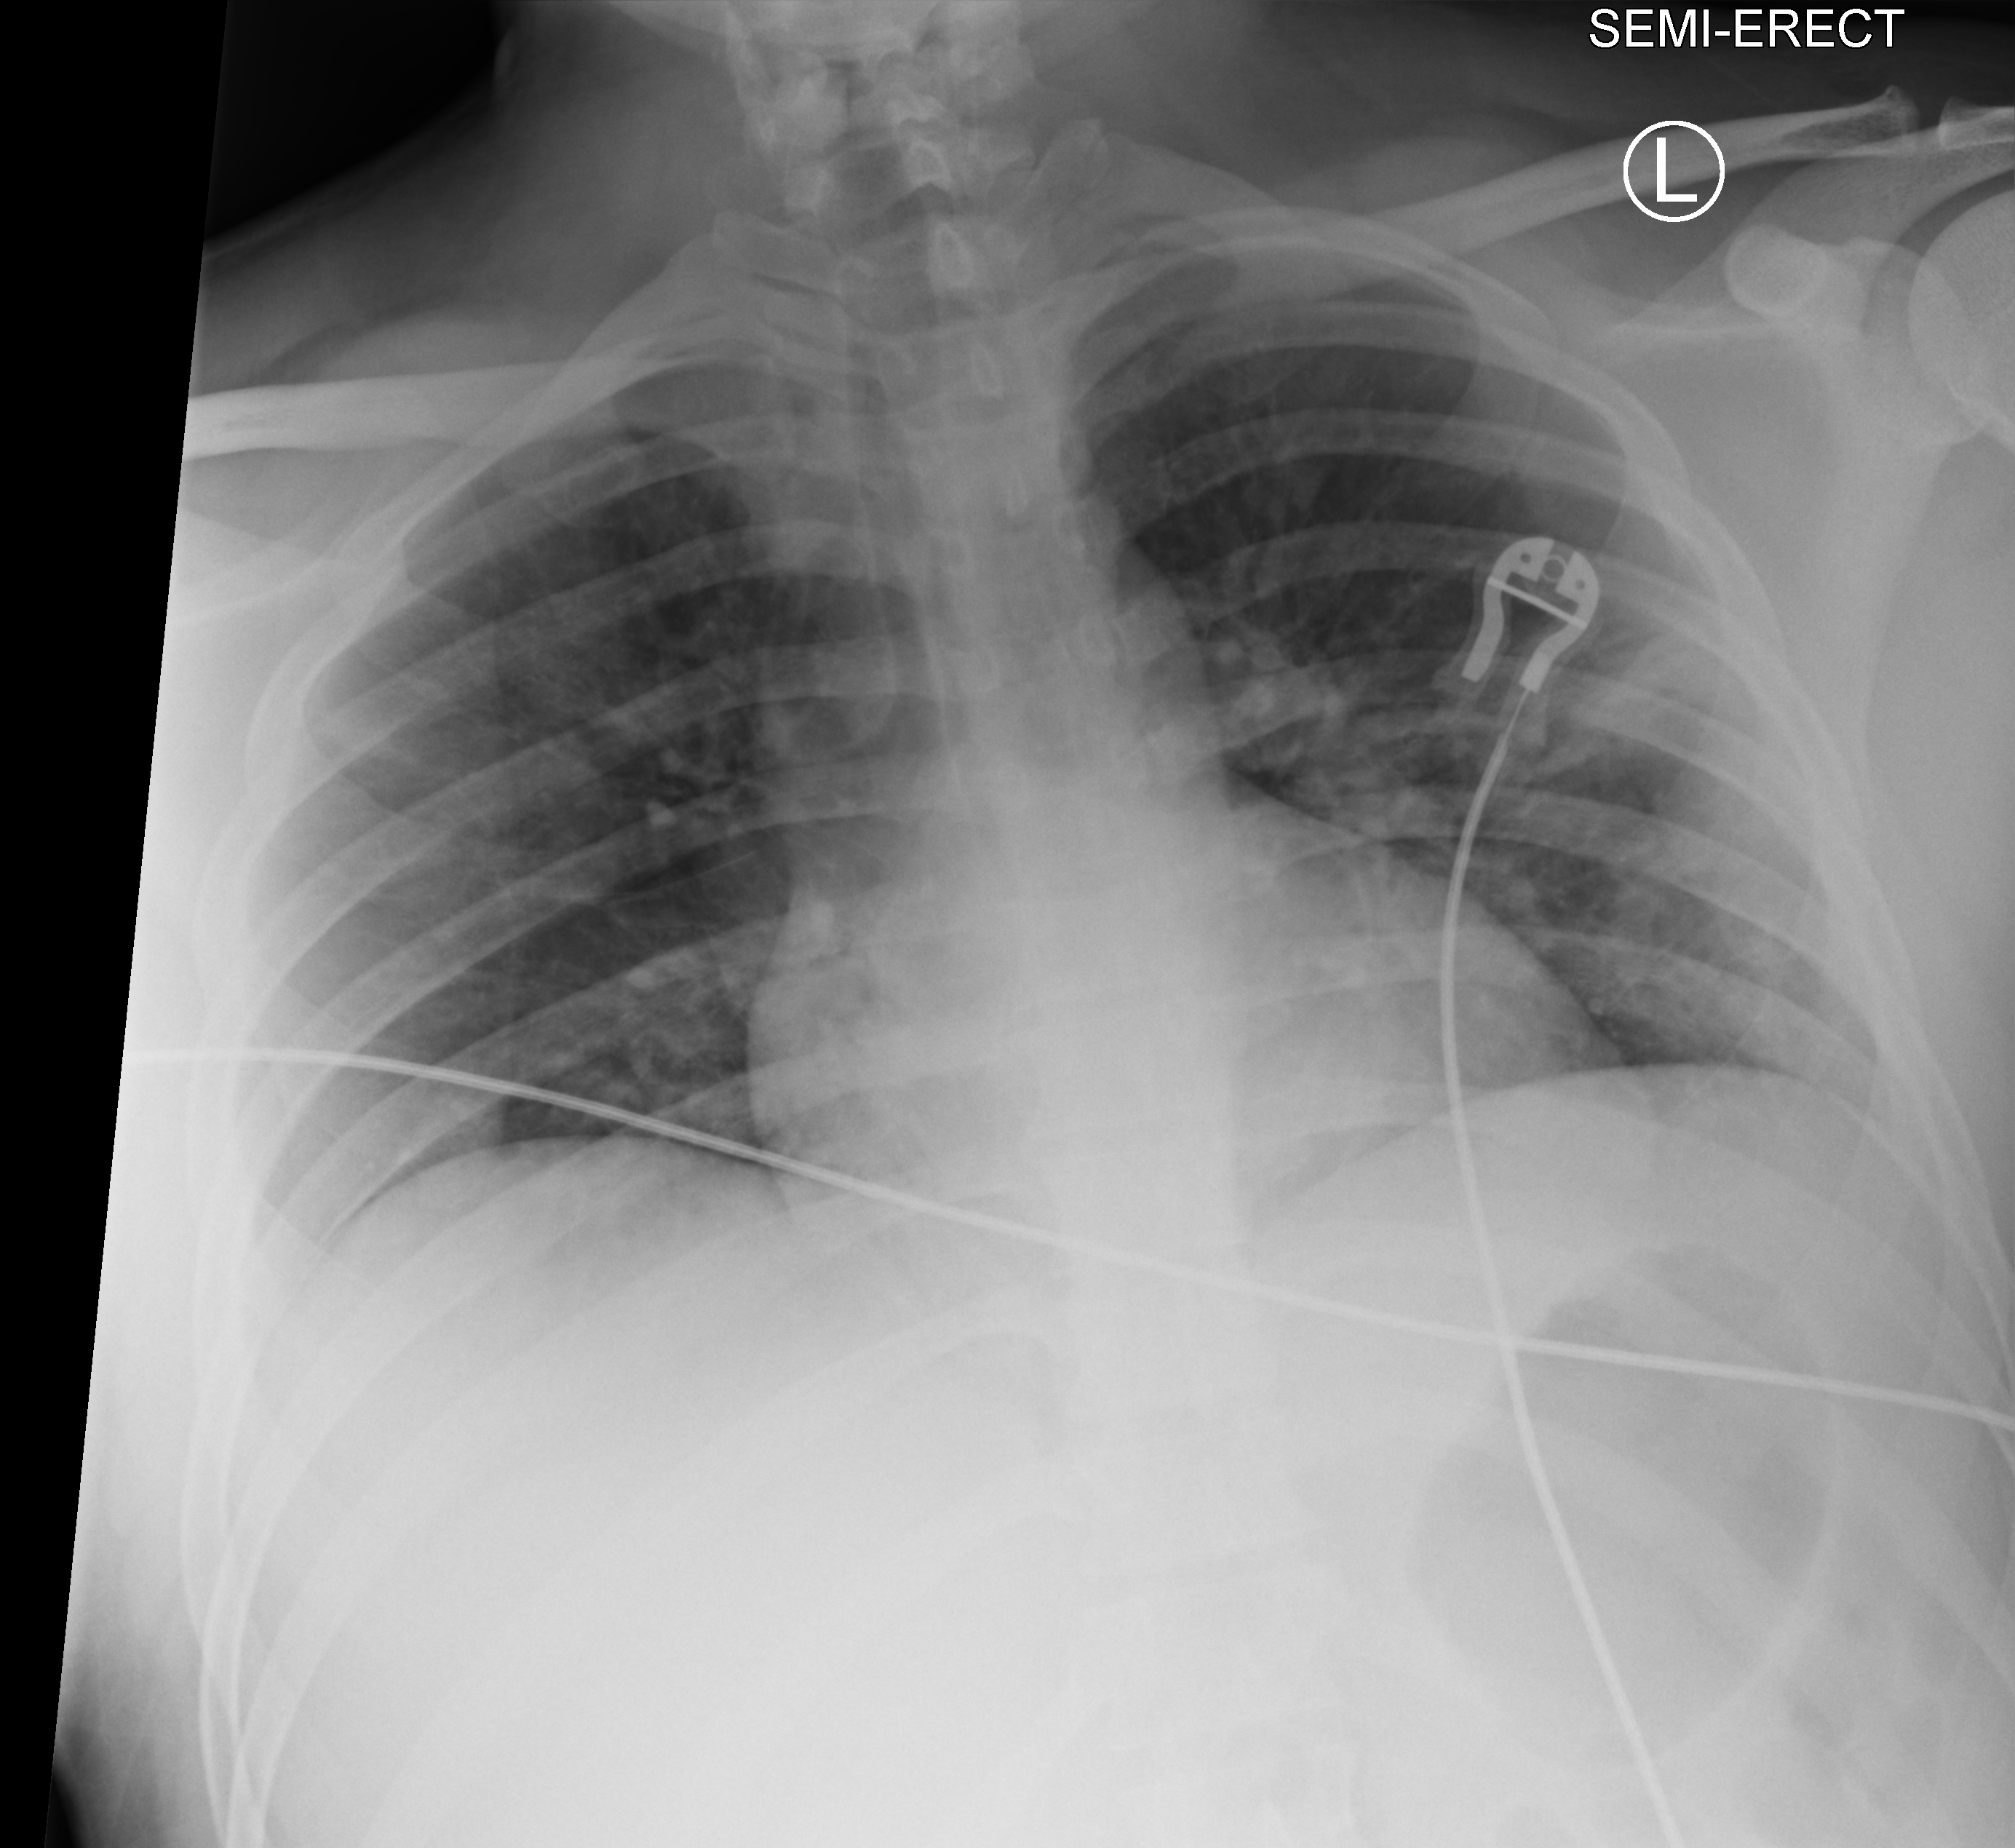
Chest X-ray (portable), anteroposterior (AP) projection. Male patient hospitalised with COVID-19, age 18–59 years.
From the hospital-stay record, not from the radiograph (when in the stay this image was taken is not recorded): mechanically ventilated during this hospital stay: no; length of hospital stay: 11 days; admitted to intensive care during this hospital stay: no.